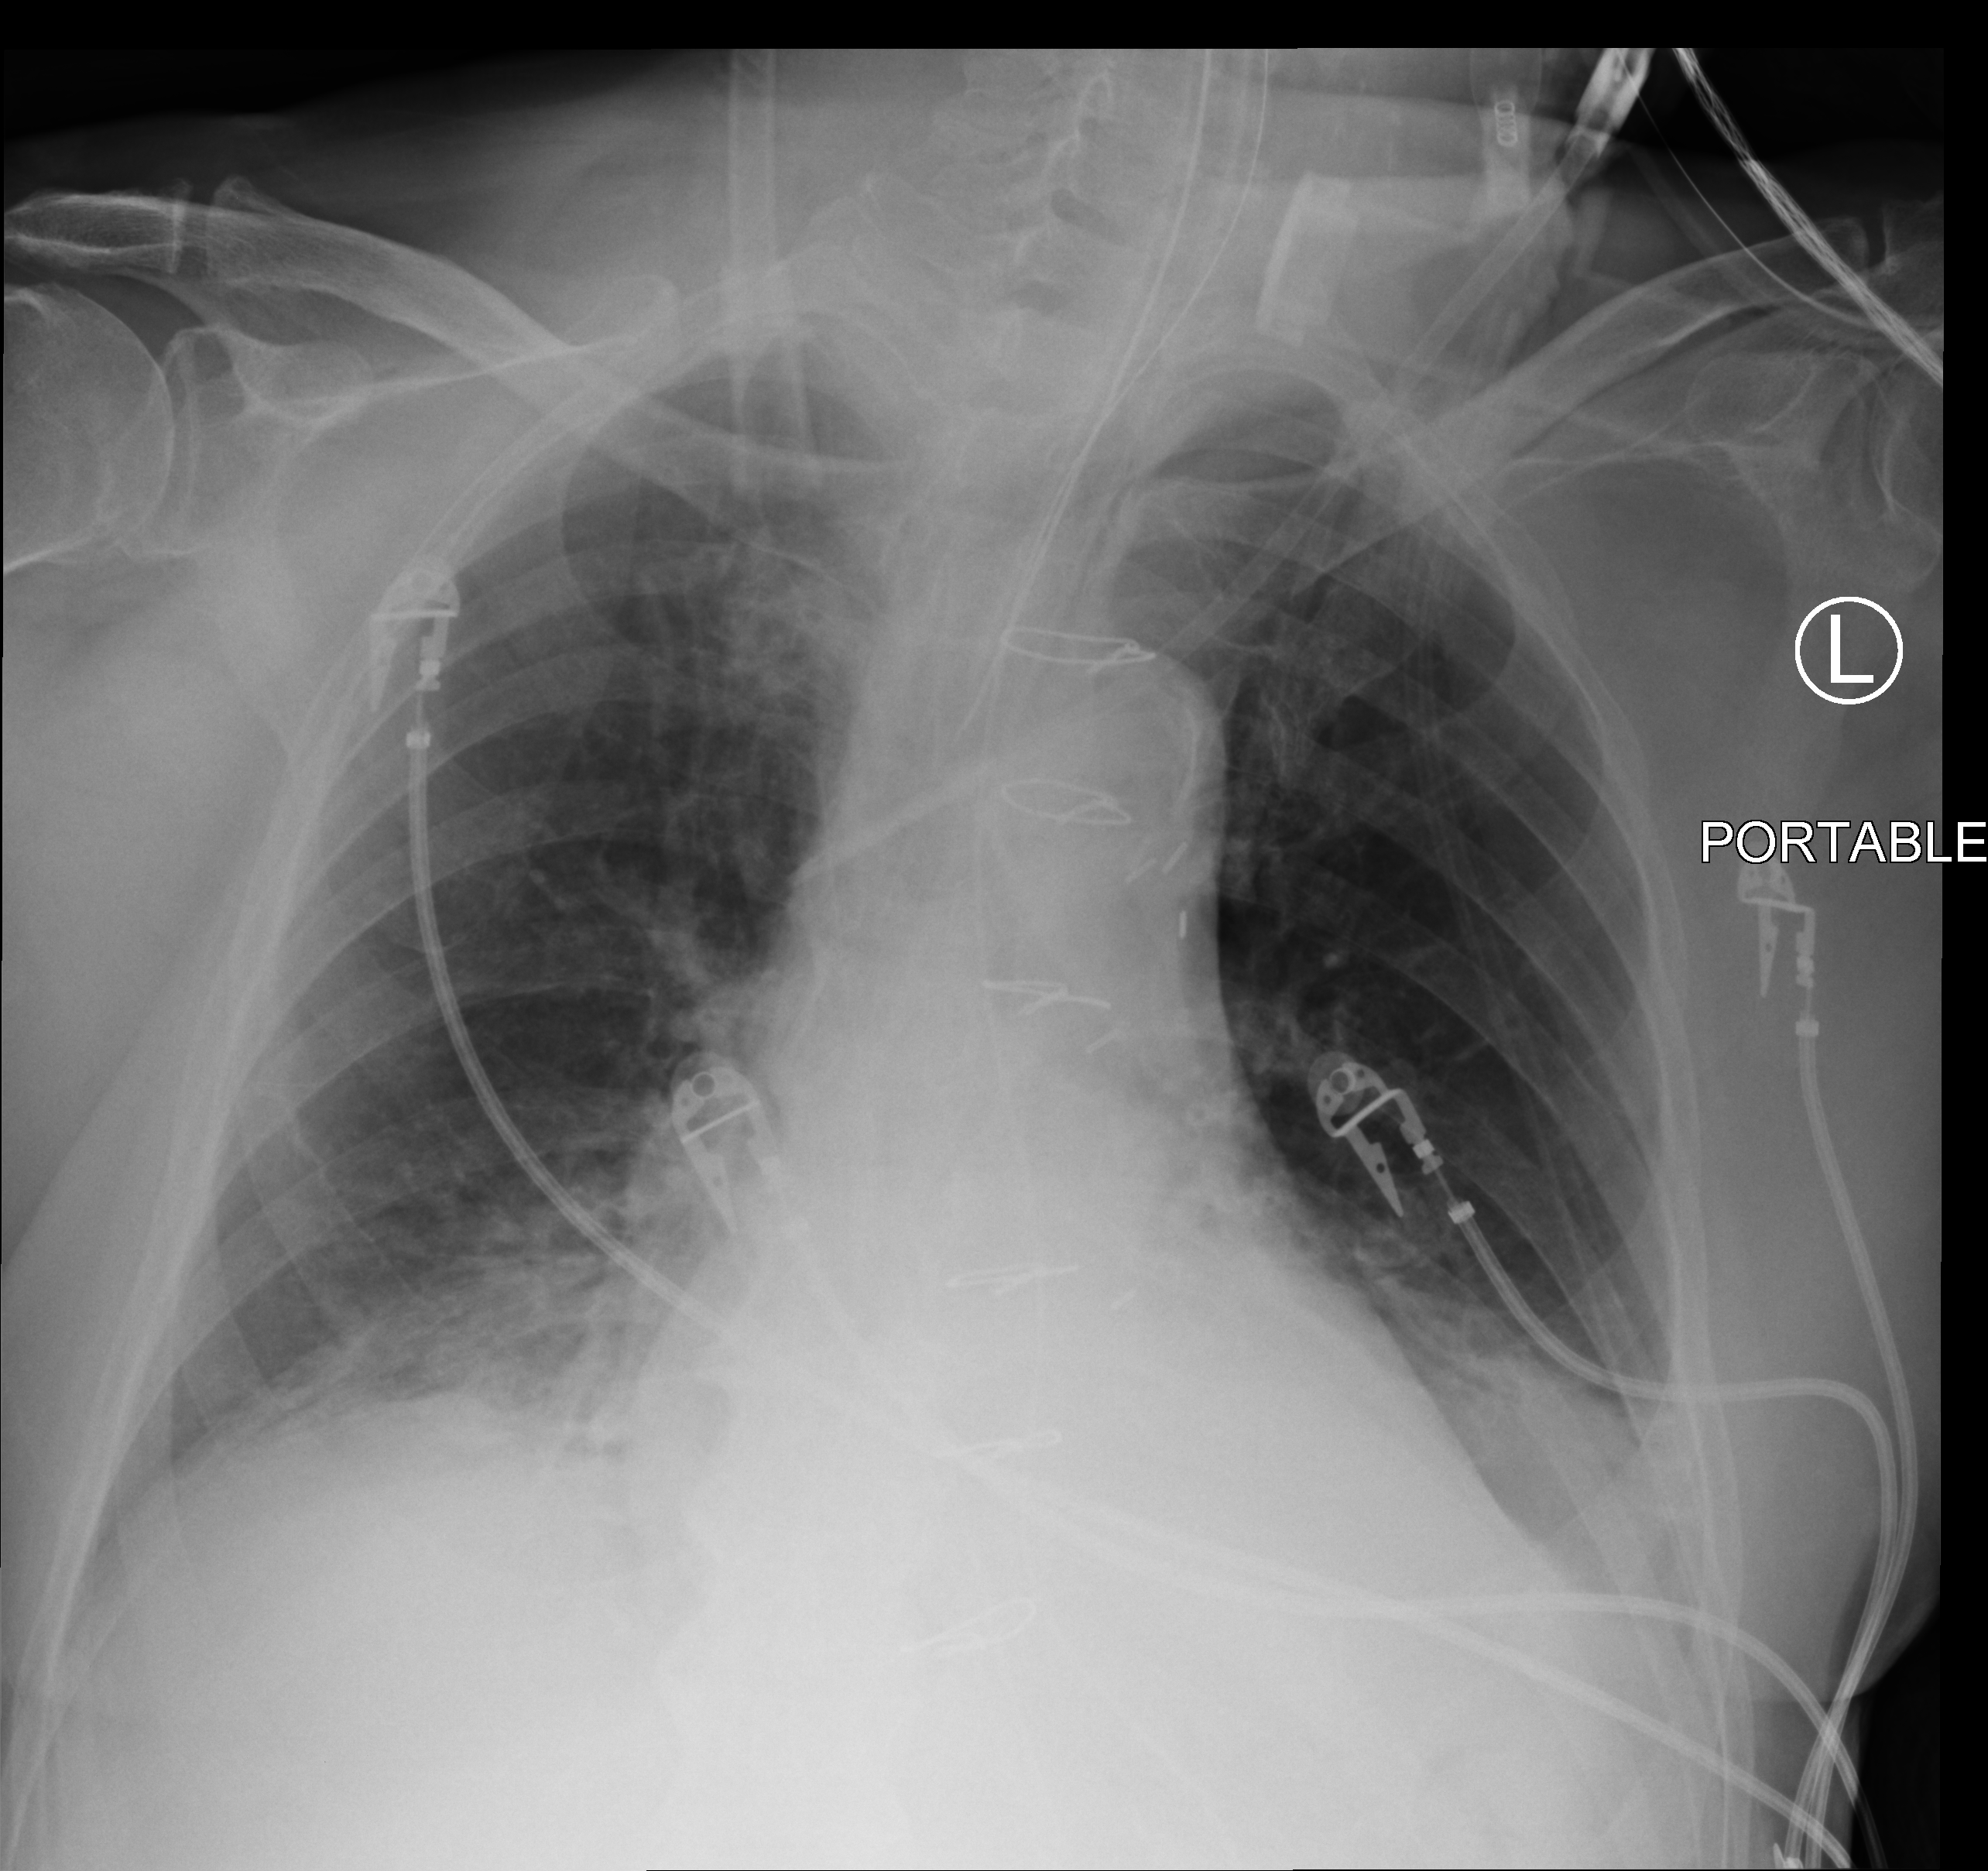
Portable chest radiograph; anteroposterior (AP) projection. Male patient hospitalised with COVID-19, age 75–90 years.
From the hospital-stay record, not from the radiograph (when in the stay this image was taken is not recorded): COPD (admission record): no; admitted to intensive care during this hospital stay: yes; other chronic lung disease (admission record): no.